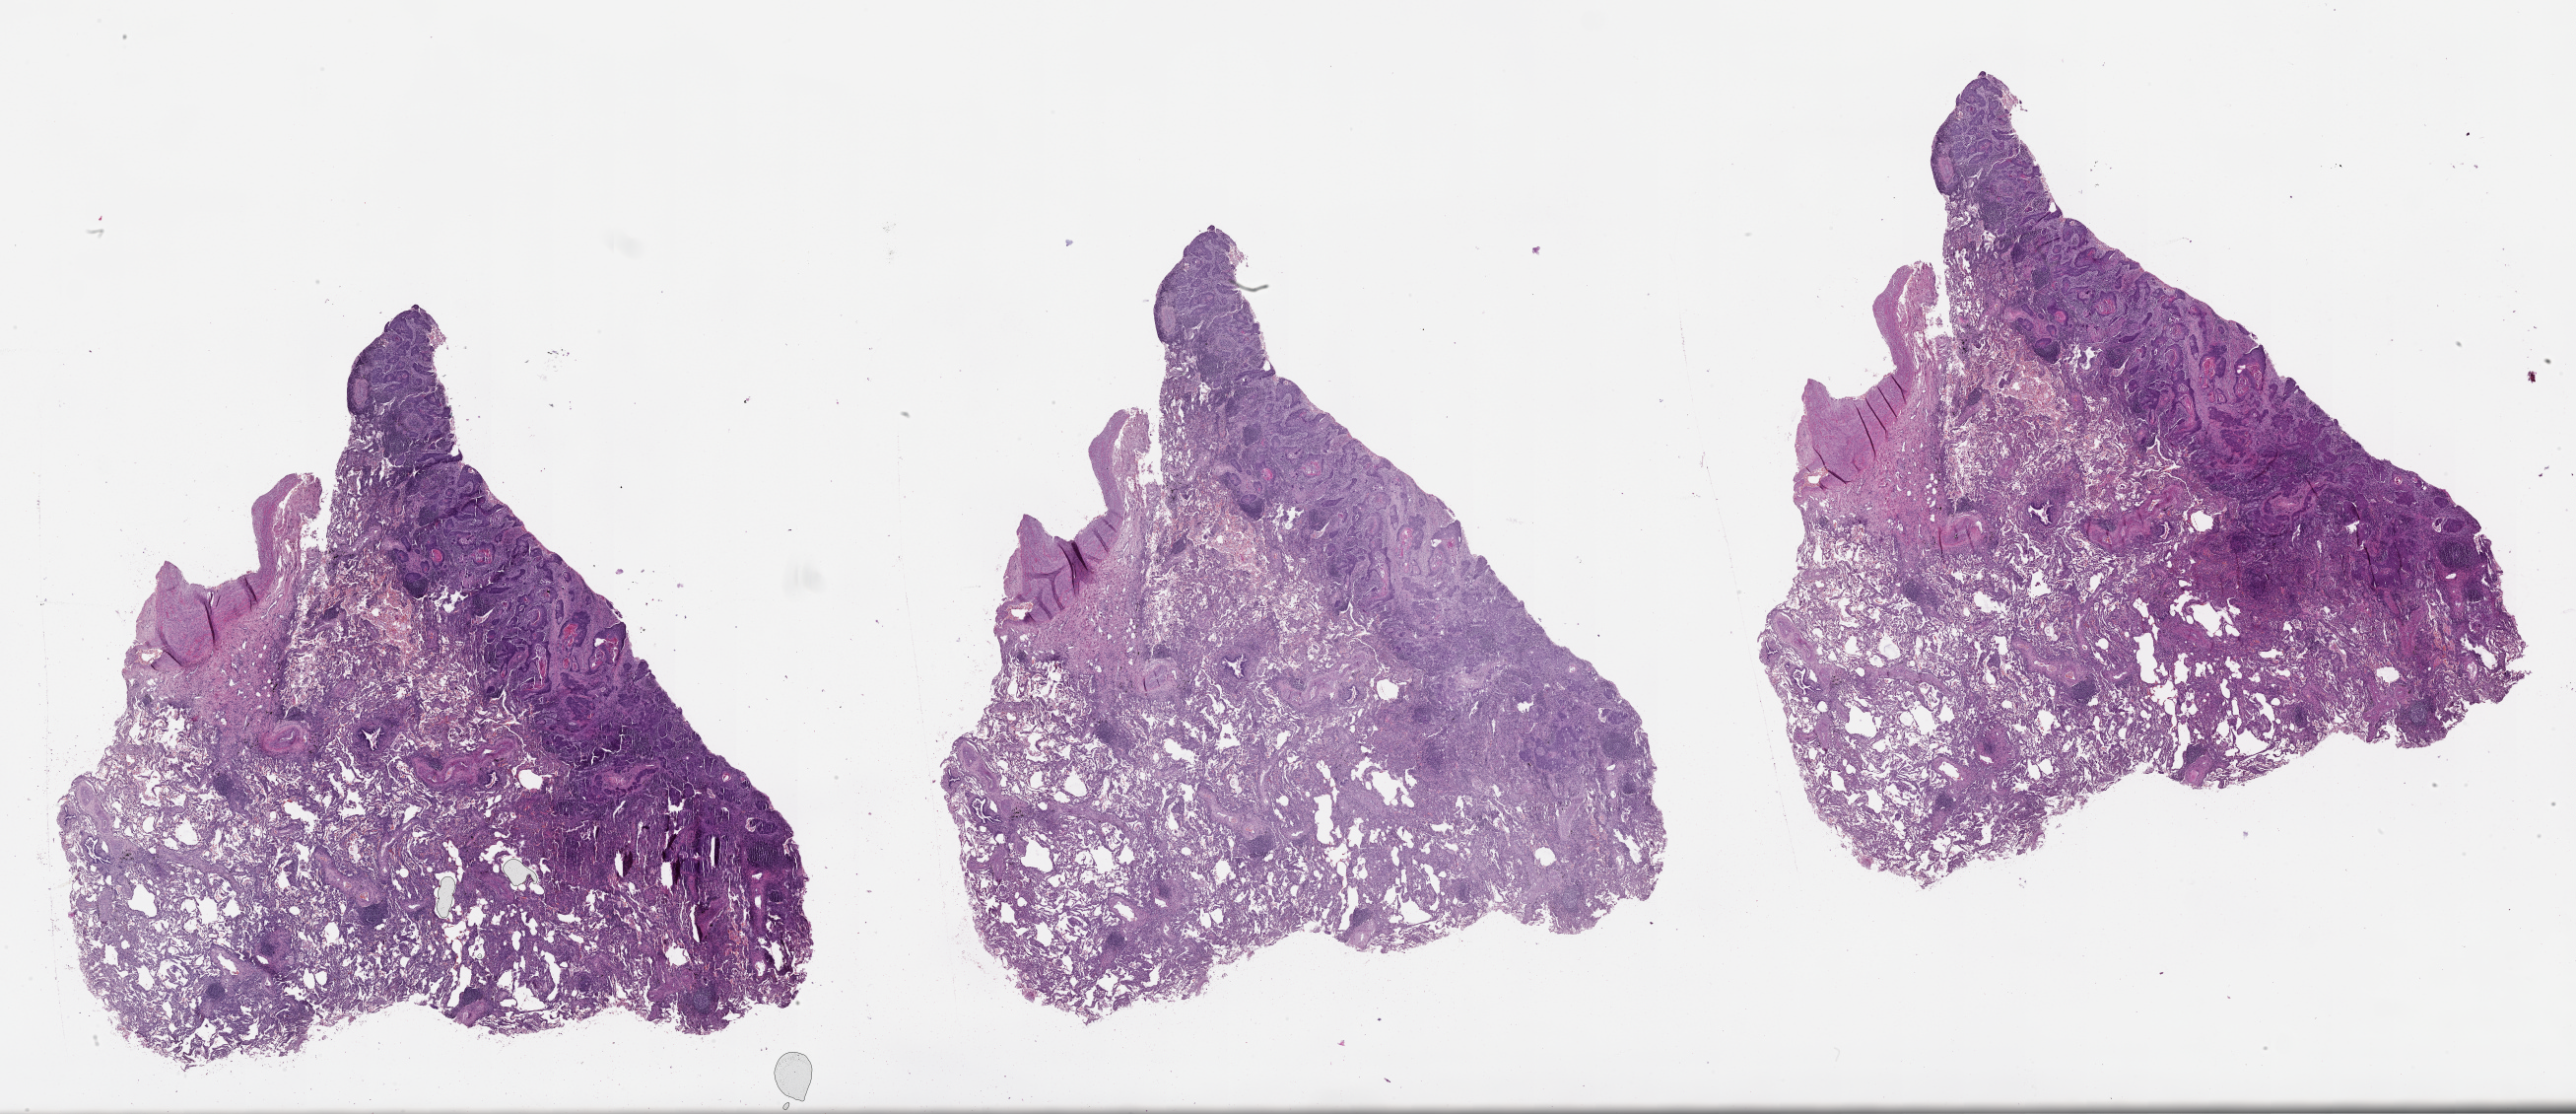
Whole-slide histology image, Hematoxylin and eosin (H&E) stained — whole scanned area (about 42.1 x 18.2 mm) shown as a low-resolution overview, tumour tissue sample, lung. 72-year-old male patient.
Patient diagnosis (cohort enrolment): squamous cell carcinoma (lung).